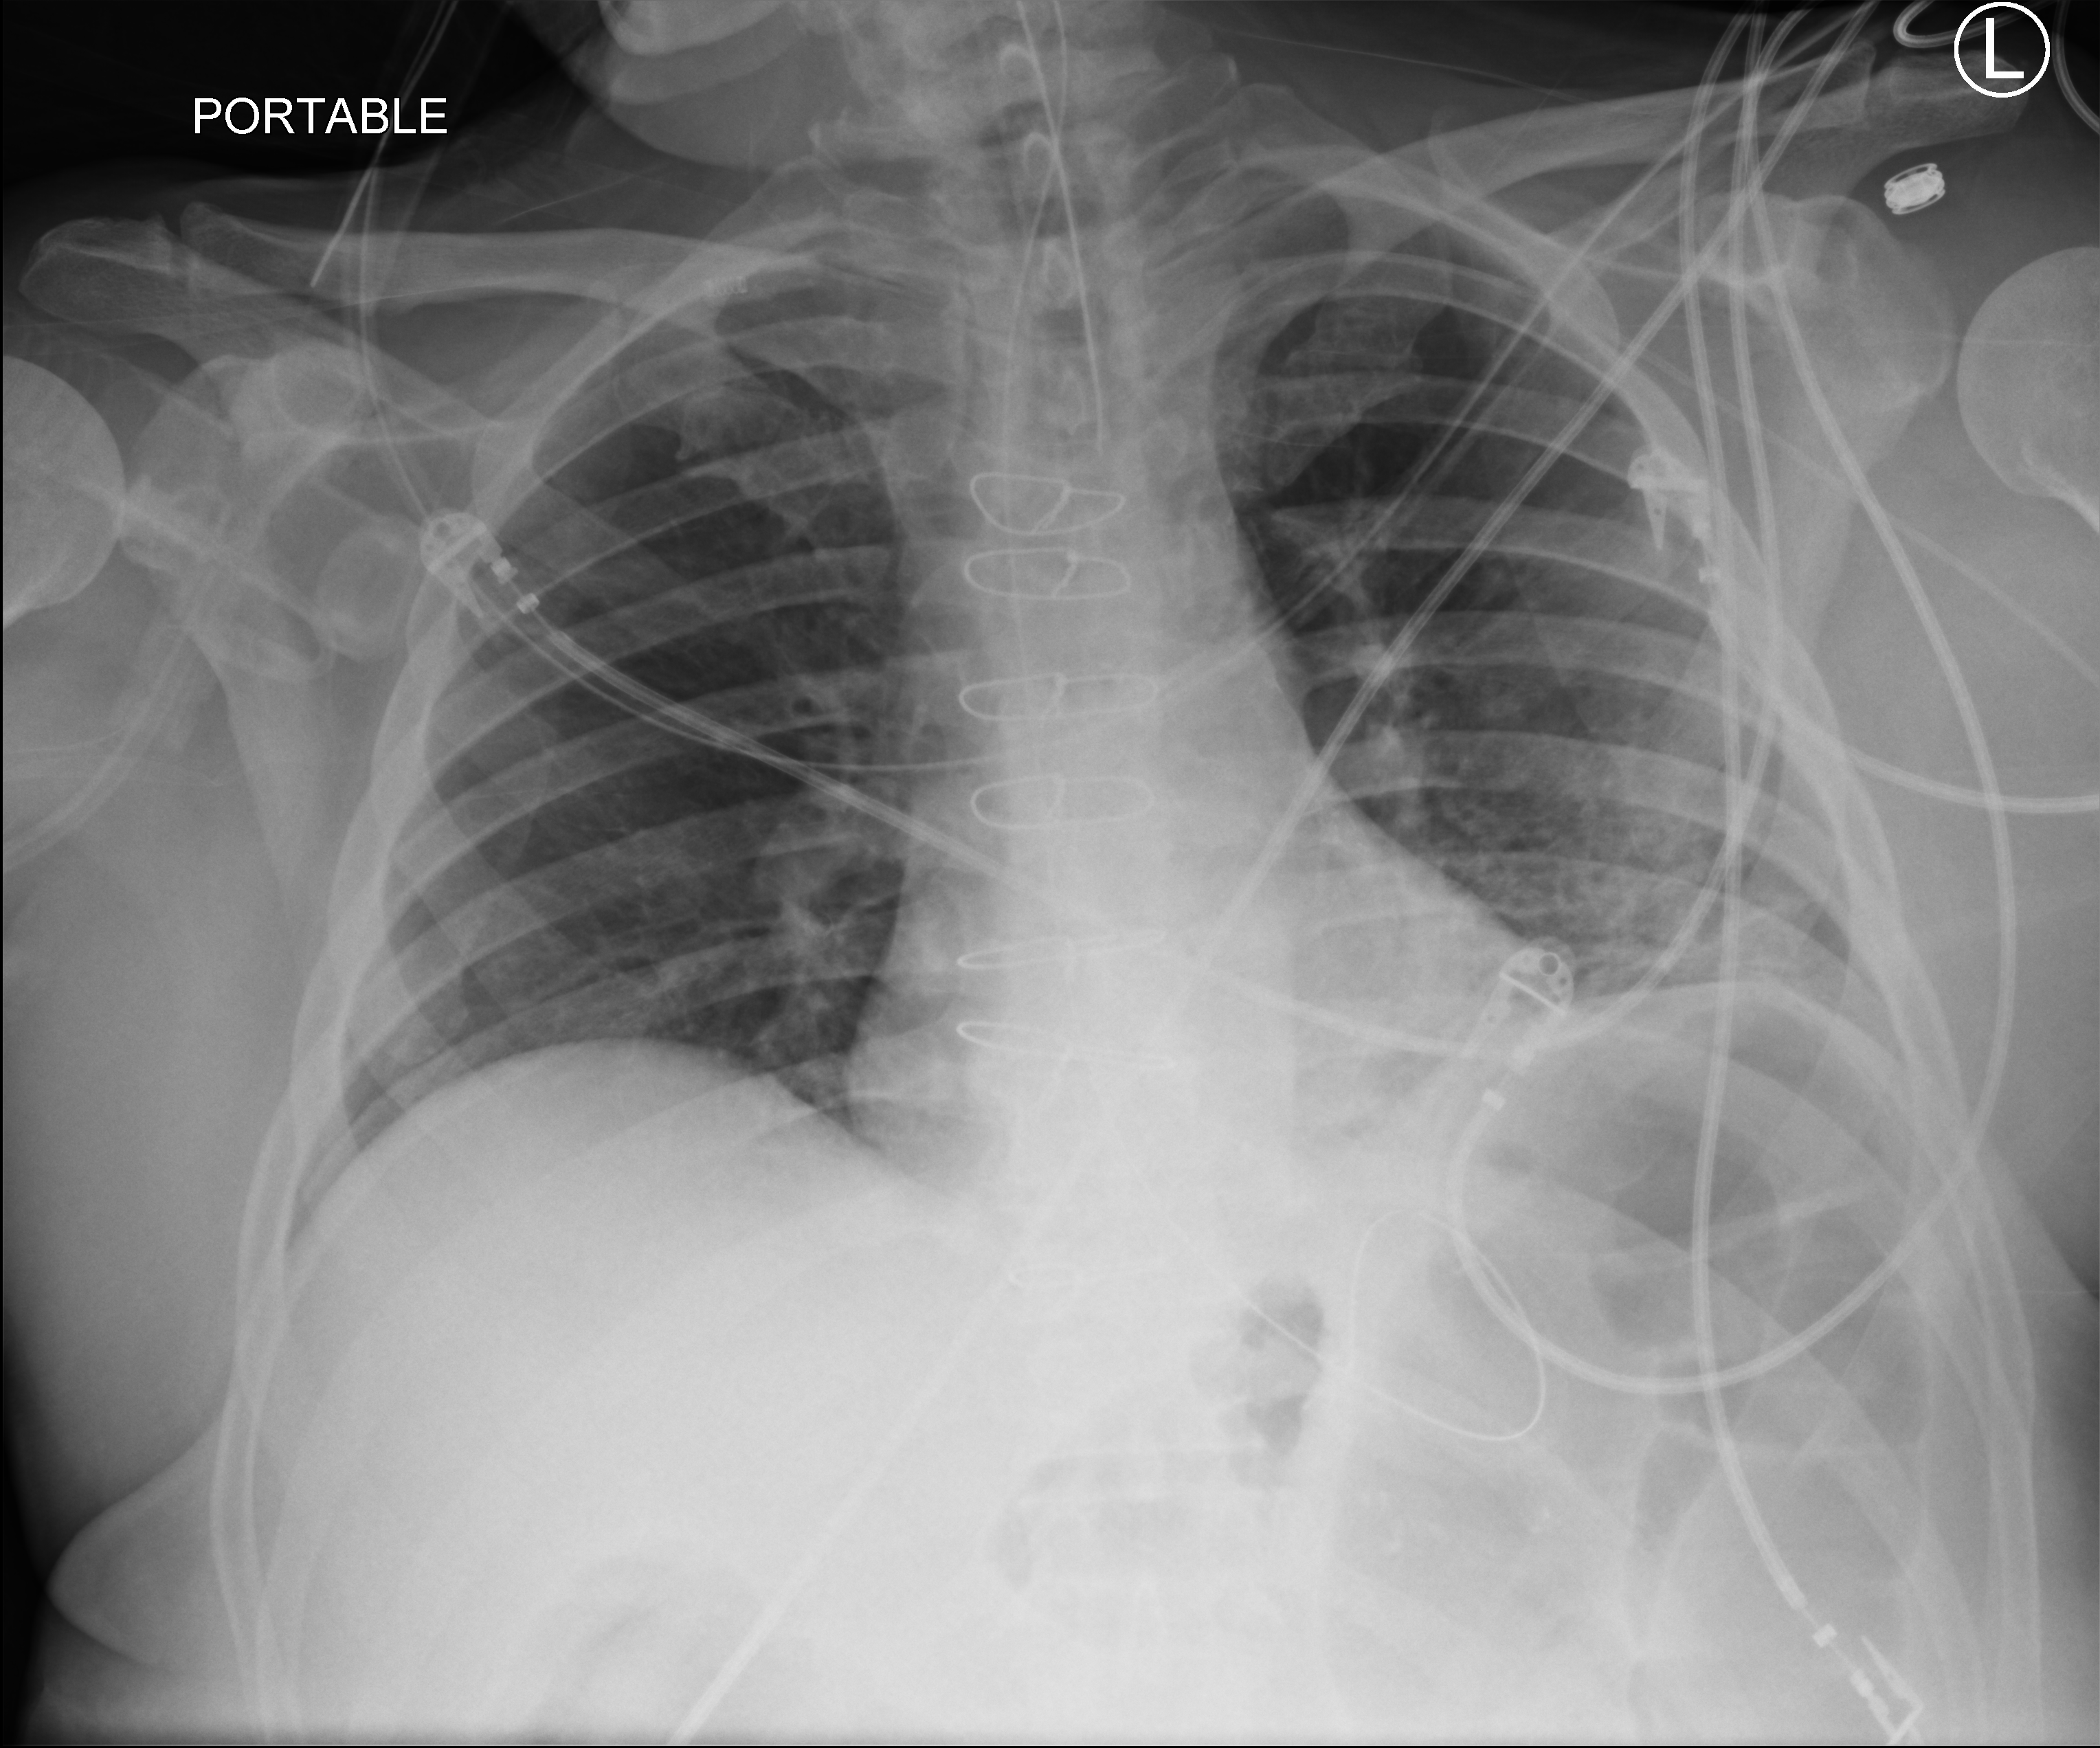
Portable chest radiograph; anteroposterior (AP) projection. Patient hospitalised with COVID-19; male, aged 60–74 years.
Hospital-stay facts (about this admission, not read from this image; timing relative to this image not recorded): mechanically ventilated during this hospital stay: yes; admitted to intensive care during this hospital stay: yes.